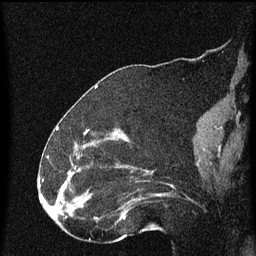
Breast MRI (dynamic contrast-enhanced), one sagittal slice; slice 27 of 60 in the series (ordered by position); dynamic contrast-enhanced series, image 2 of 4 at this slice position (ordered by acquisition); 1.5 T; TE 4.2 ms, TR 8 ms; 2 mm slice thickness; 256 × 256 image matrix, field of view 180 × 180 mm. Female patient, age 52 years.
Structures marked on this image (semi-automatically segmented with operator editing):
- analysis volume of interest (the breast-tissue region the enhancement analysis was run in; not a lesion): bounding box <73,148,172,219> (left, top, right, bottom; pixels)
- tumour enhancement mask (voxels above the 70 % enhancement threshold inside the analysis volume of interest): <75,172,124,217>